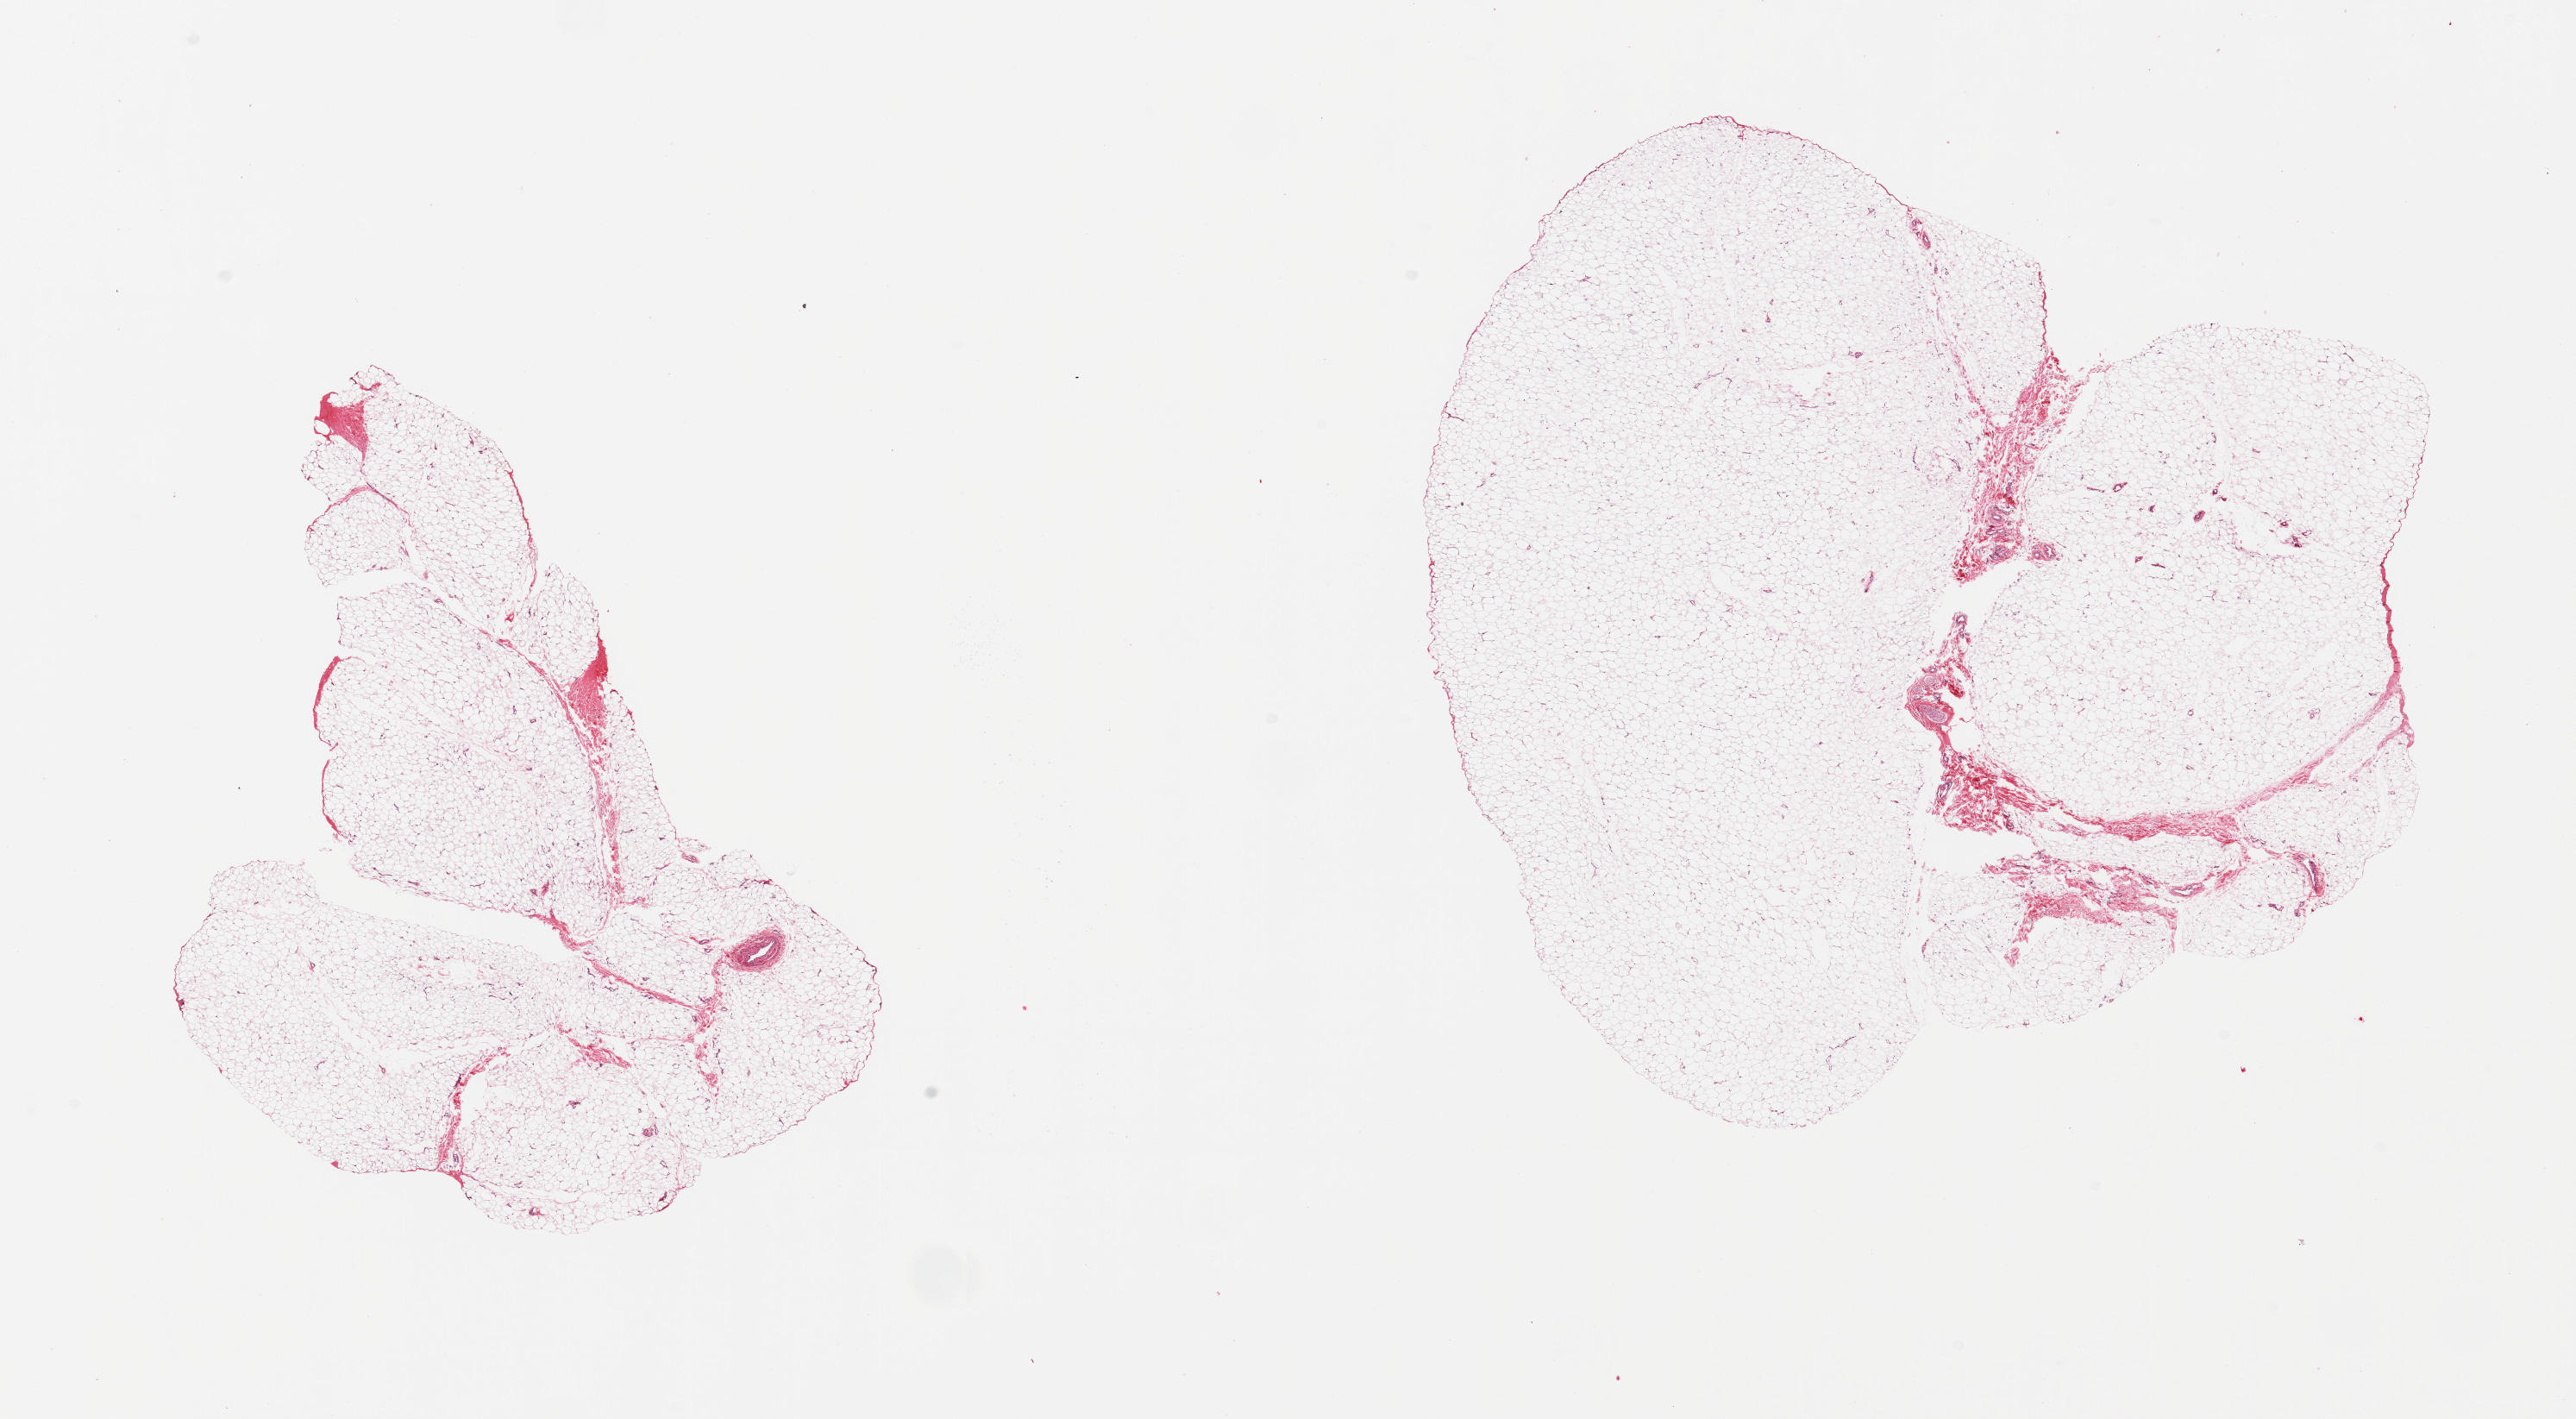
Hematoxylin and eosin (H&E) whole-slide image — shown as a low-resolution overview of the whole scanned area (about 23.6 x 13.0 mm); PAXgene-fixed paraffin-embedded (PFPE) section; target tissue: adipose tissue; tissue donor sample. Male donor.
* reviewer comment on this tissue sample: 2 pieces; mature fat with small contribution of fibrous/nerve/vascular tissue